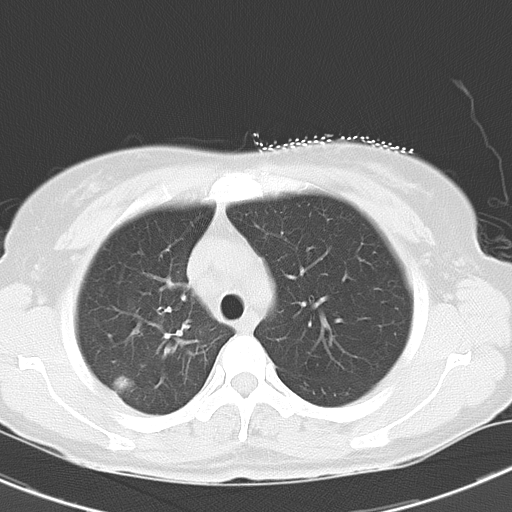
Chest CT, one axial slice. Position 23 of 29 along the scan axis. Reconstruction kernel B70f. Lung window (W 1500 / L -600 HU). 8 mm slice thickness. 512 × 512 image matrix. Female patient, age 47 years. From the clinical record (not read from this slice): clinical TNM (as recorded): T1c N3 M0.
Outlined on this slice (rectangle marked by the reading radiologist):
- lung tumour (recorded histology: adenocarcinoma): bounding box (x1, y1, x2, y2) in pixels: (111, 374, 138, 392)